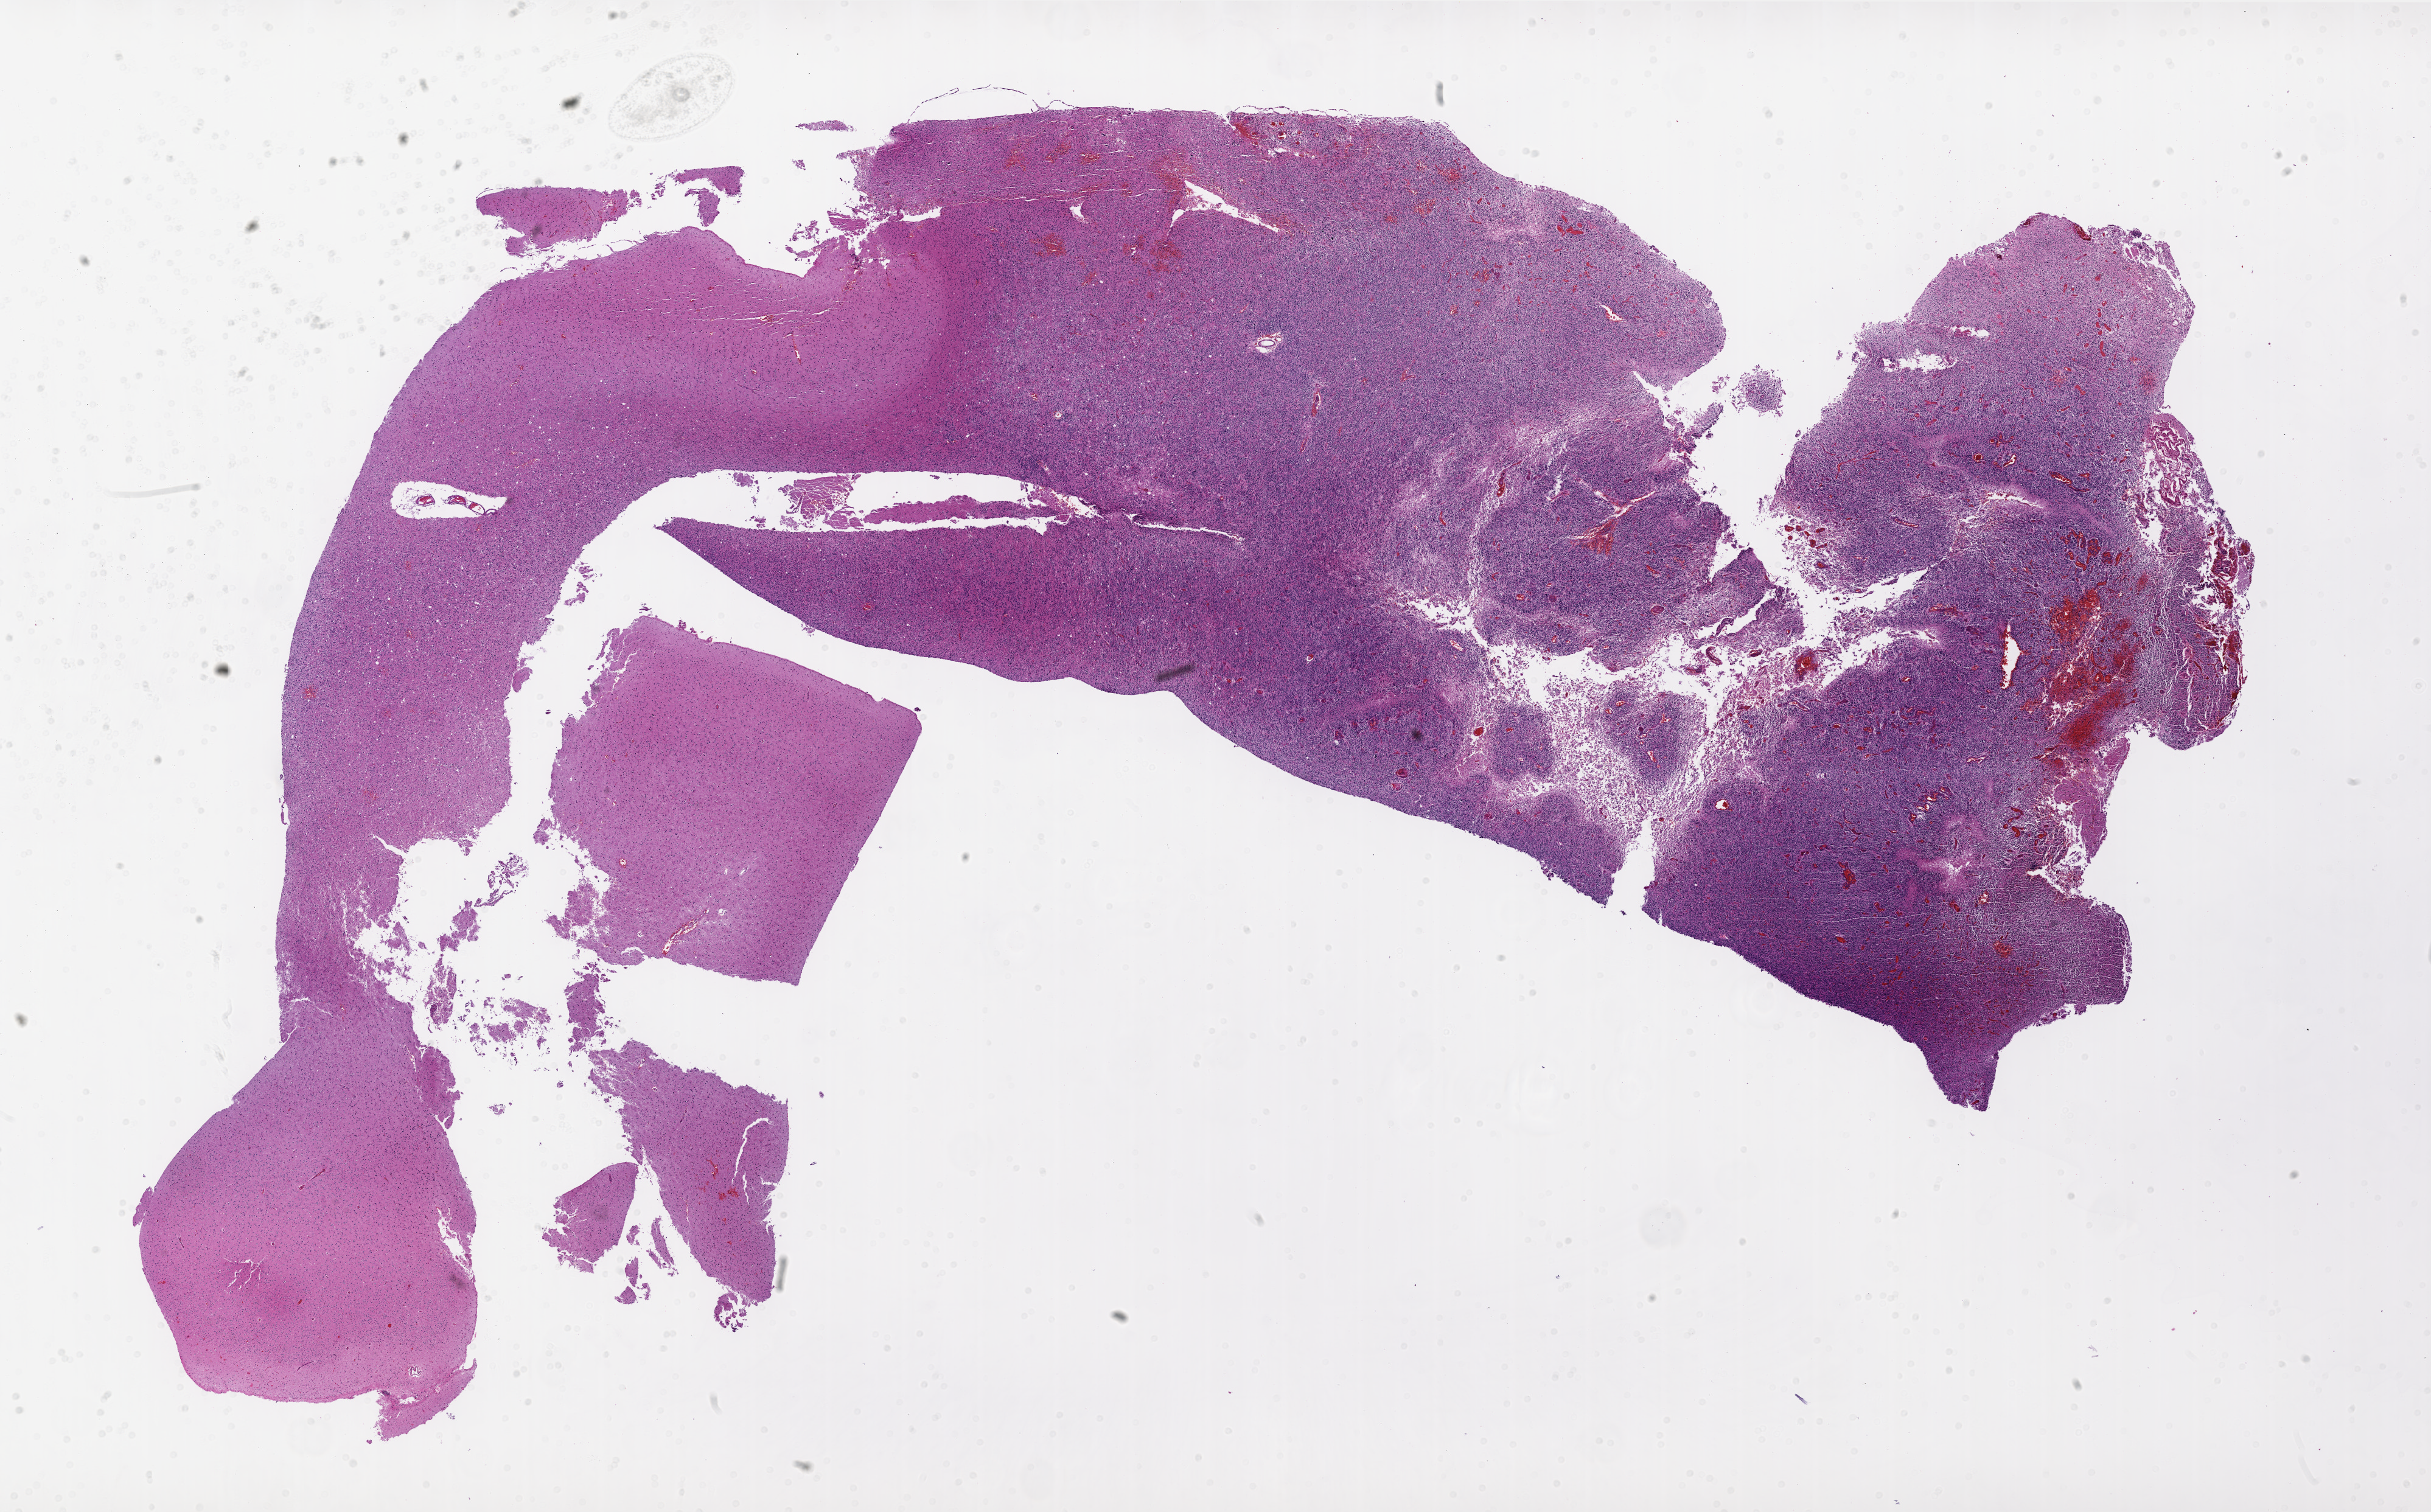
Whole-slide histology image, H&E-stained, low-resolution overview of the scanned area, about 32.0 x 19.9 mm (slide scanned at 20x); FFPE section; sample: primary tumour, brain. Male, age 49 years at initial diagnosis.
Pathologic diagnosis: Glioblastoma.